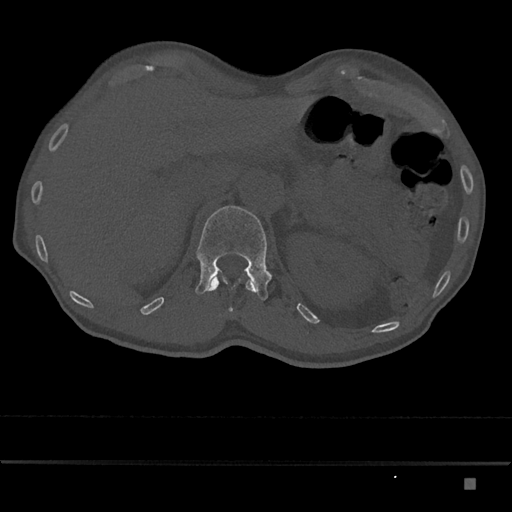
CT including the spine, one axial slice; position 569 of 797 along the scan axis; 120 kVp; bone window (W 1800 / L 400 HU); 0.5 mm slice thickness; 512 × 512 image matrix, field of view 390 × 390 mm. Patient: male, 72 years. Case-level facts recorded for this patient, not image findings: primary cancer: prostate.
Outlined on this slice (semi-automatic segmentation, software-assisted and operator-edited):
- L1 vertebra: bounding box (x1, y1, x2, y2) in pixels: (195, 205, 272, 300)
- T12 vertebra: (206, 275, 256, 312)